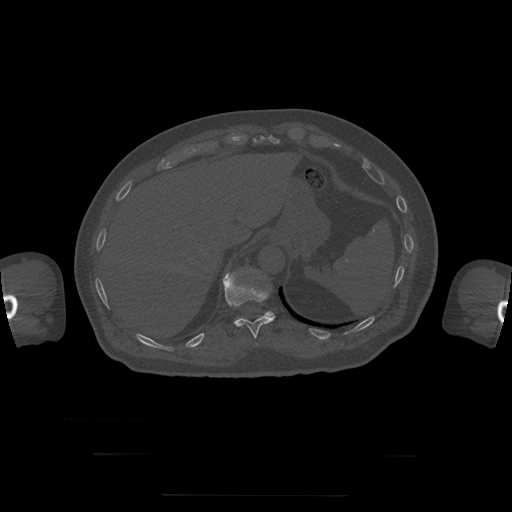
CT including the spine, one axial slice. Position 94 of 397 along the scan axis. Bone window (W 1800 / L 400 HU). 1.25 mm slice thickness. 512 × 512 image matrix, field of view 510 × 510 mm. Patient age 73 years. From the clinical record (not read from this slice): primary cancer: prostate.
Outlined on this slice (semi-automatic segmentation, software-assisted and operator-edited):
- T11 vertebra: bounding box (x1, y1, x2, y2) in pixels: (223, 271, 276, 339)
- T12 vertebra: (237, 312, 274, 320)